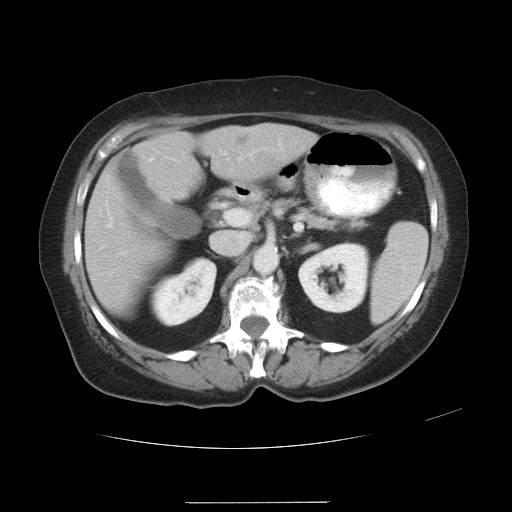
Contrast-enhanced abdominal CT, one axial slice. Position 16 of 32 along the scan axis. Reconstruction kernel STANDARD. 120 kVp. Intravenous contrast given. Soft-tissue window (W 400 / L 40 HU). 7.5 mm slice thickness. 512 × 512 image matrix. Female patient, age 65 years. Case-level facts recorded for this patient, not image findings: diagnosis: colorectal cancer liver metastases, imaged before liver resection; multiple liver metastases: yes; largest metastasis: 1.7 cm; chemotherapy before resection: no.
Outlined on this slice (manually delineated by an expert):
- liver: bounding box <86,124,313,310> (left, top, right, bottom; pixels)
- planned liver remnant (the part of the liver to remain after resection): <86,135,206,311>
- portal vein (with intrahepatic branches): <107,156,244,227>
- liver metastasis: <235,136,249,147>